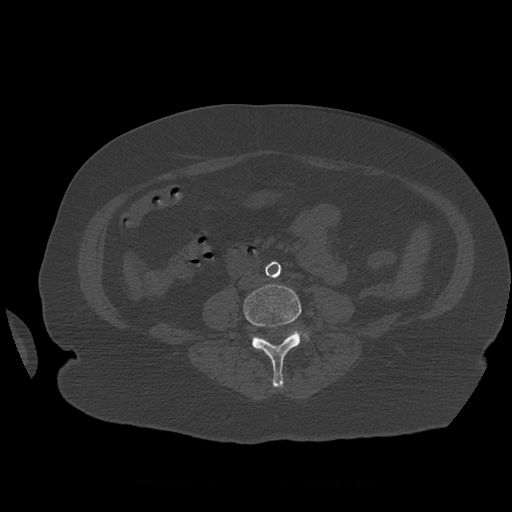
CT including the spine, one axial slice; position 202 of 399 along the scan axis; reconstruction kernel STANDARD; 120 kVp; bone window (W 1800 / L 400 HU); 1.25 mm slice thickness; 512 × 512 image matrix, field of view 404 × 404 mm. Patient age 81 years. Case-level facts recorded for this patient, not image findings: primary cancer: renal.
Structures marked on this image (semi-automatically segmented with operator editing):
- L4 vertebra: bounding box <244,284,304,388> (left, top, right, bottom; pixels)
- L5 vertebra: <252,330,308,345>